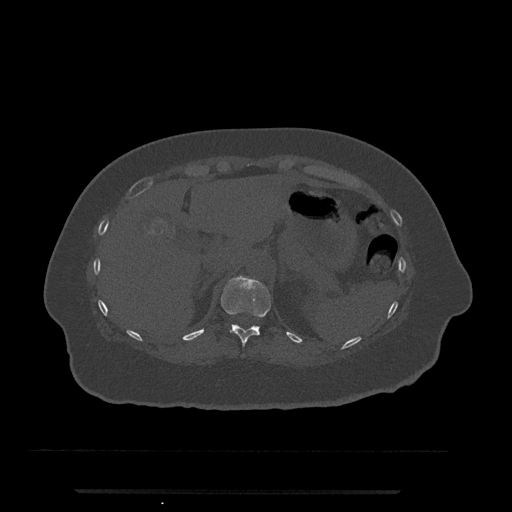
CT including the spine, one axial slice; slice 221 of 797 in the series (ordered by position); 120 kVp; bone window (W 1800 / L 400 HU); 0.5 mm slice thickness; 512 × 512 image matrix, field of view 440 × 440 mm. Patient: female, 51 years. Case-level facts recorded for this patient, not image findings: primary cancer: neuro; vertebrae with lytic lesions (as recorded): T8.
Outlined on this slice (semi-automatically segmented with operator editing):
- T11 vertebra: bounding box <221,275,271,347> (left, top, right, bottom; pixels)